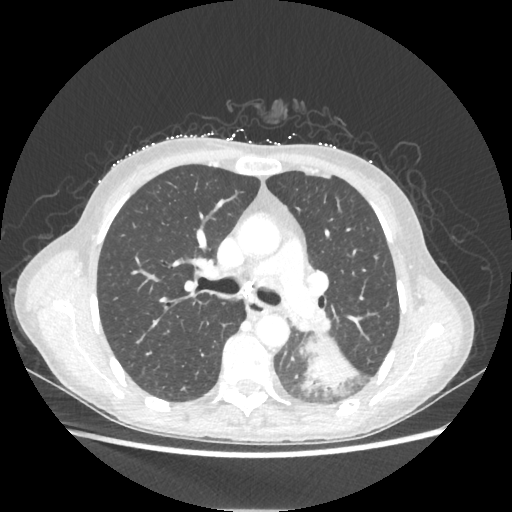
Chest CT, one axial slice. Slice 133 of 221 in the series (ordered by position). Reconstruction kernel STANDARD. Lung window (W 1500 / L -600 HU). 1.25 mm slice thickness. 512 × 512 image matrix. Patient: female, 53 years. From the clinical record (not read from this slice): clinical TNM (as recorded): T3 N0 M0.
Annotated regions visible in this slice (bounding box drawn by a radiologist):
- lung tumour (recorded histology: adenocarcinoma): bounding box <301,335,359,394> (left, top, right, bottom; pixels)